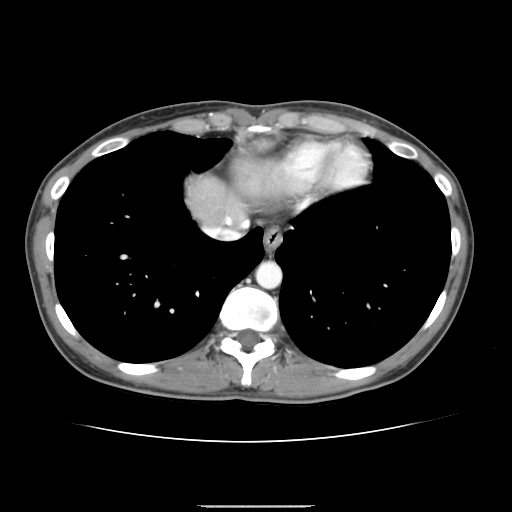
Contrast-enhanced abdominal CT, one axial slice; position 136 of 150 along the scan axis; intravenous contrast given; soft-tissue window (W 400 / L 40 HU); 2.5 mm slice thickness; 512 × 512 image matrix, field of view 324 × 324 mm. Female patient, age 32 years. Case-level facts recorded for this patient, not image findings: diagnosis: colorectal cancer liver metastases, imaged before liver resection; multiple liver metastases: yes; largest metastasis: 0.7 cm; chemotherapy before resection: yes.
Annotated regions visible in this slice (outlined manually by an expert reader):
- hepatic veins: bounding box (x1, y1, x2, y2) in pixels: (219, 233, 225, 239)
- liver: (189, 181, 243, 227)
- planned liver remnant (the part of the liver to remain after resection): (189, 180, 242, 227)
- portal vein (with intrahepatic branches): (226, 217, 231, 224)